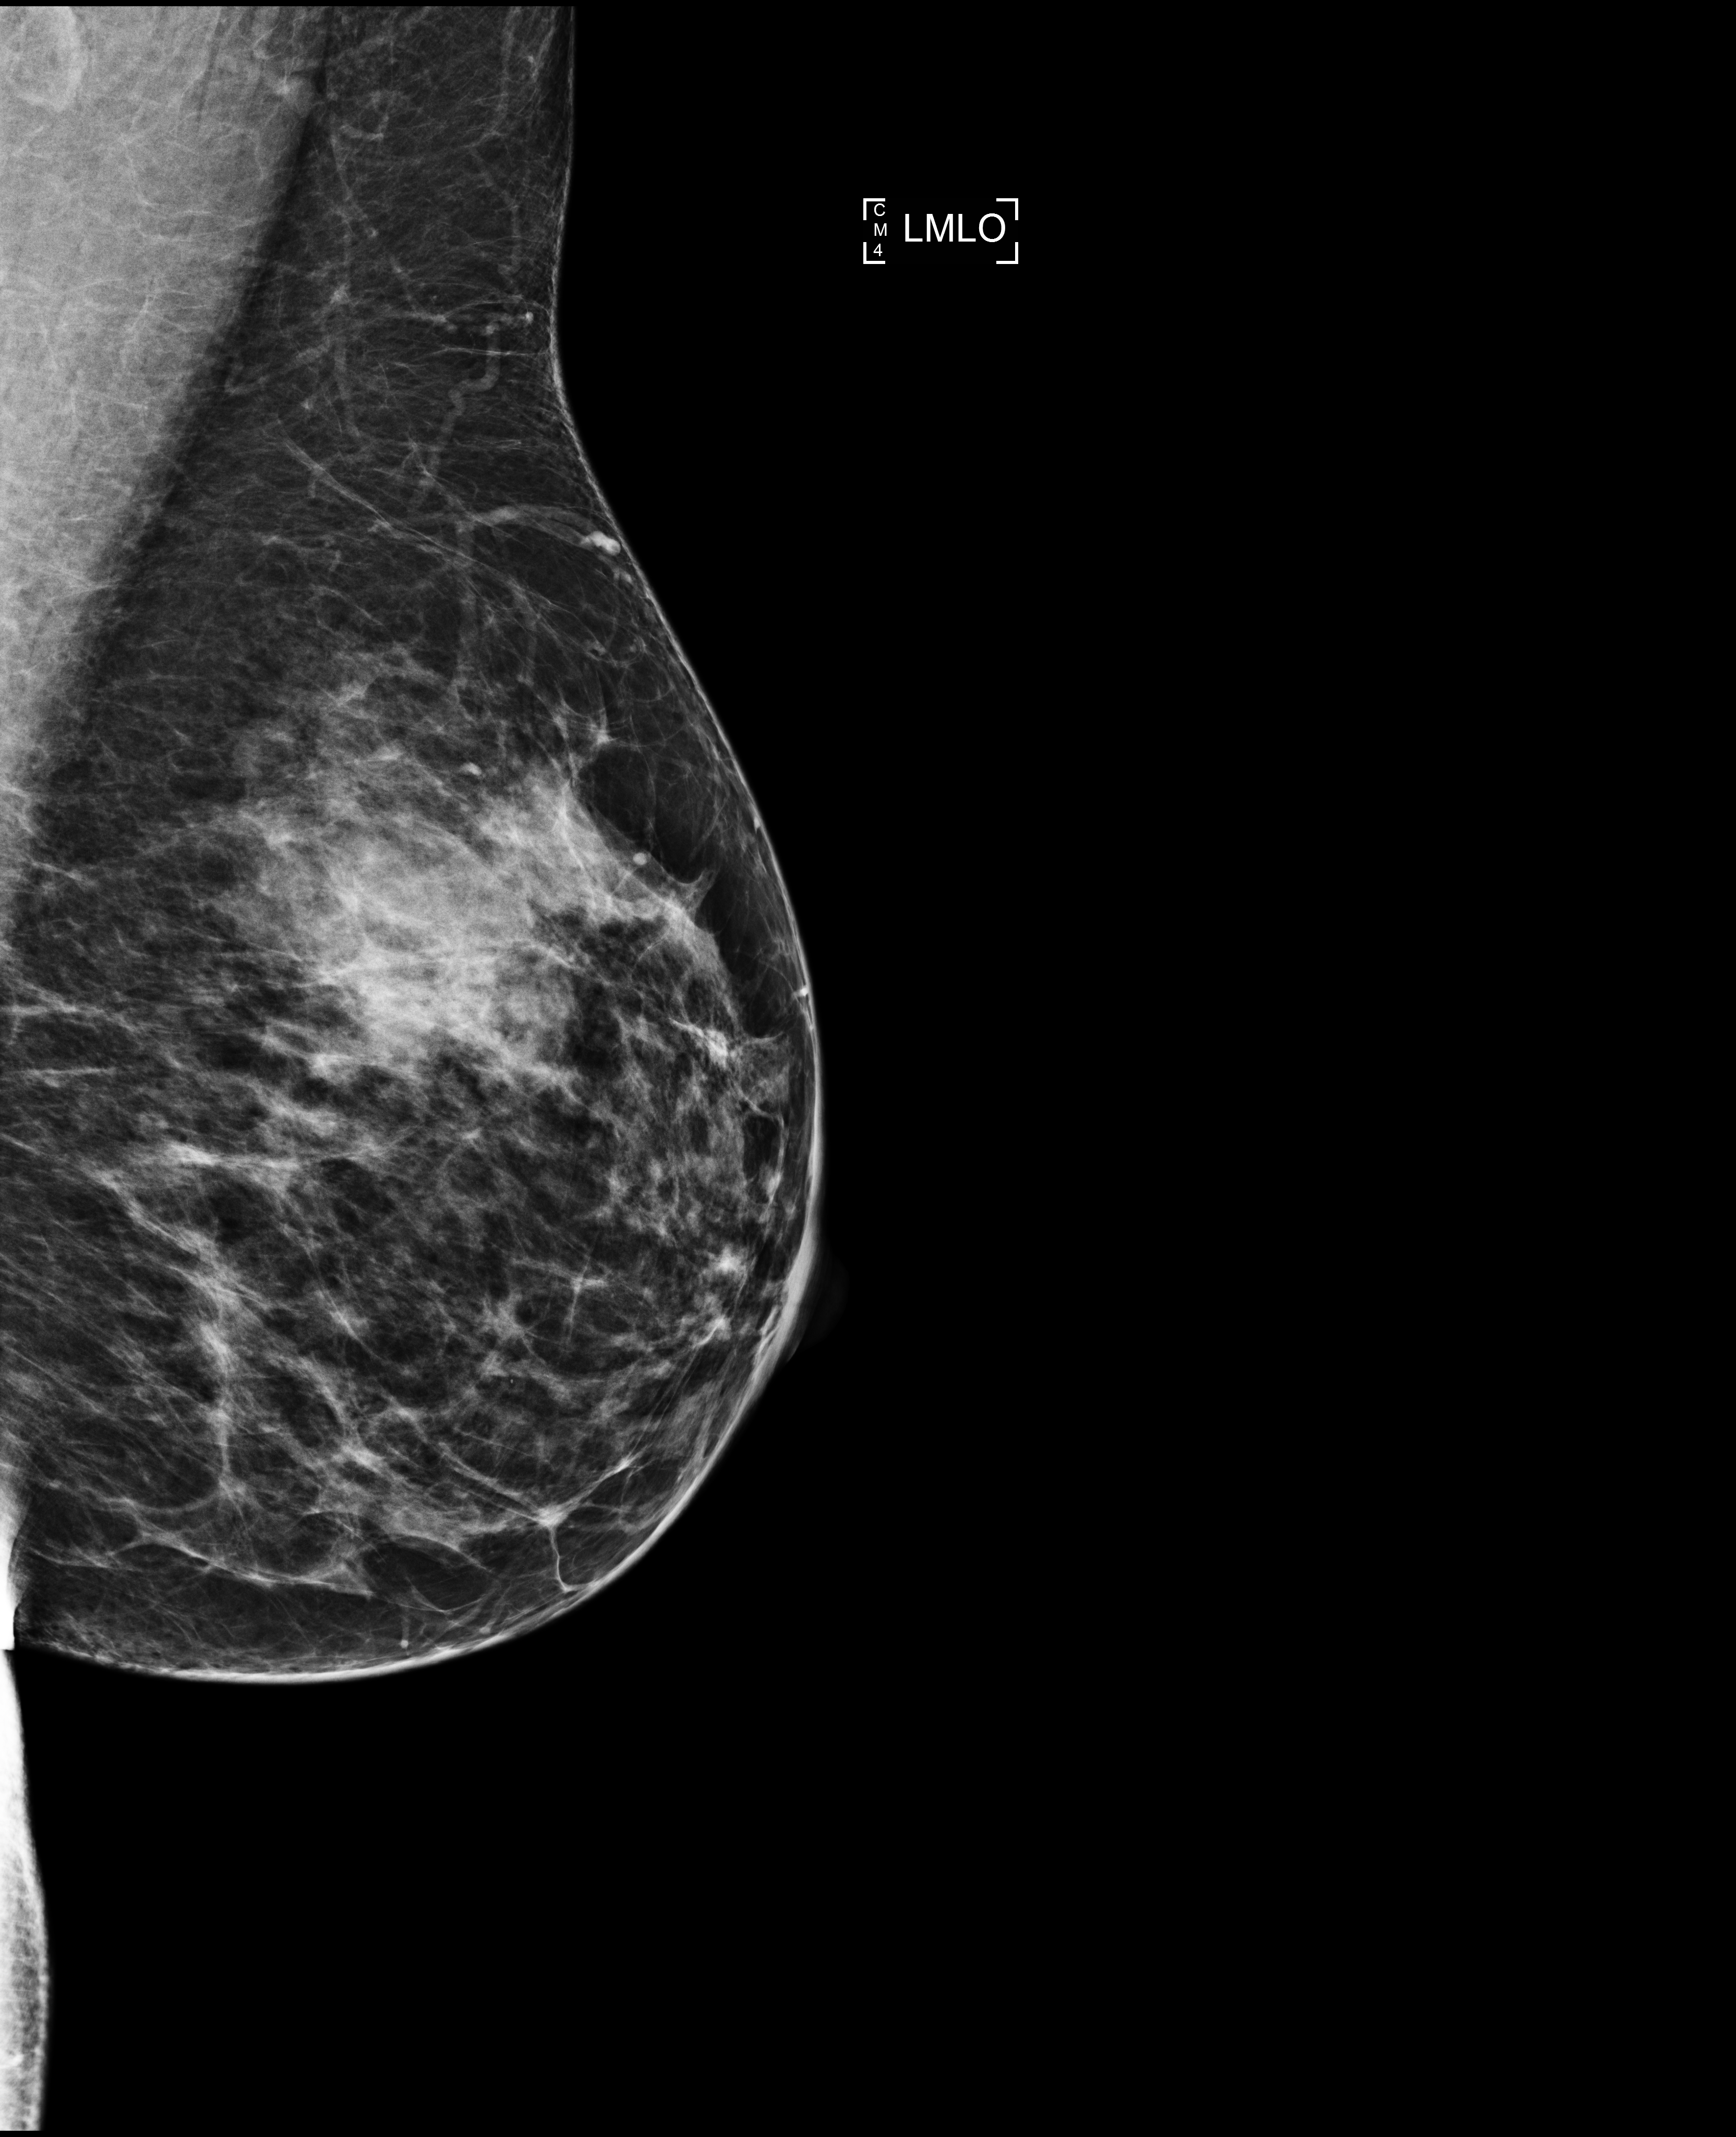
Full-field digital mammogram (FFDM), left breast, mediolateral oblique (MLO) view, annual screening mammography examination, compressed breast thickness 69 mm, system: Selenia Dimensions. Patient: female, 46 years.
BI-RADS breast density category at the screening exam (both breasts, scale 1–4): 3. Final BI-RADS assessment for this screening round (tomosynthesis exam, both breasts): category 1. Recall: no recall after this screen.